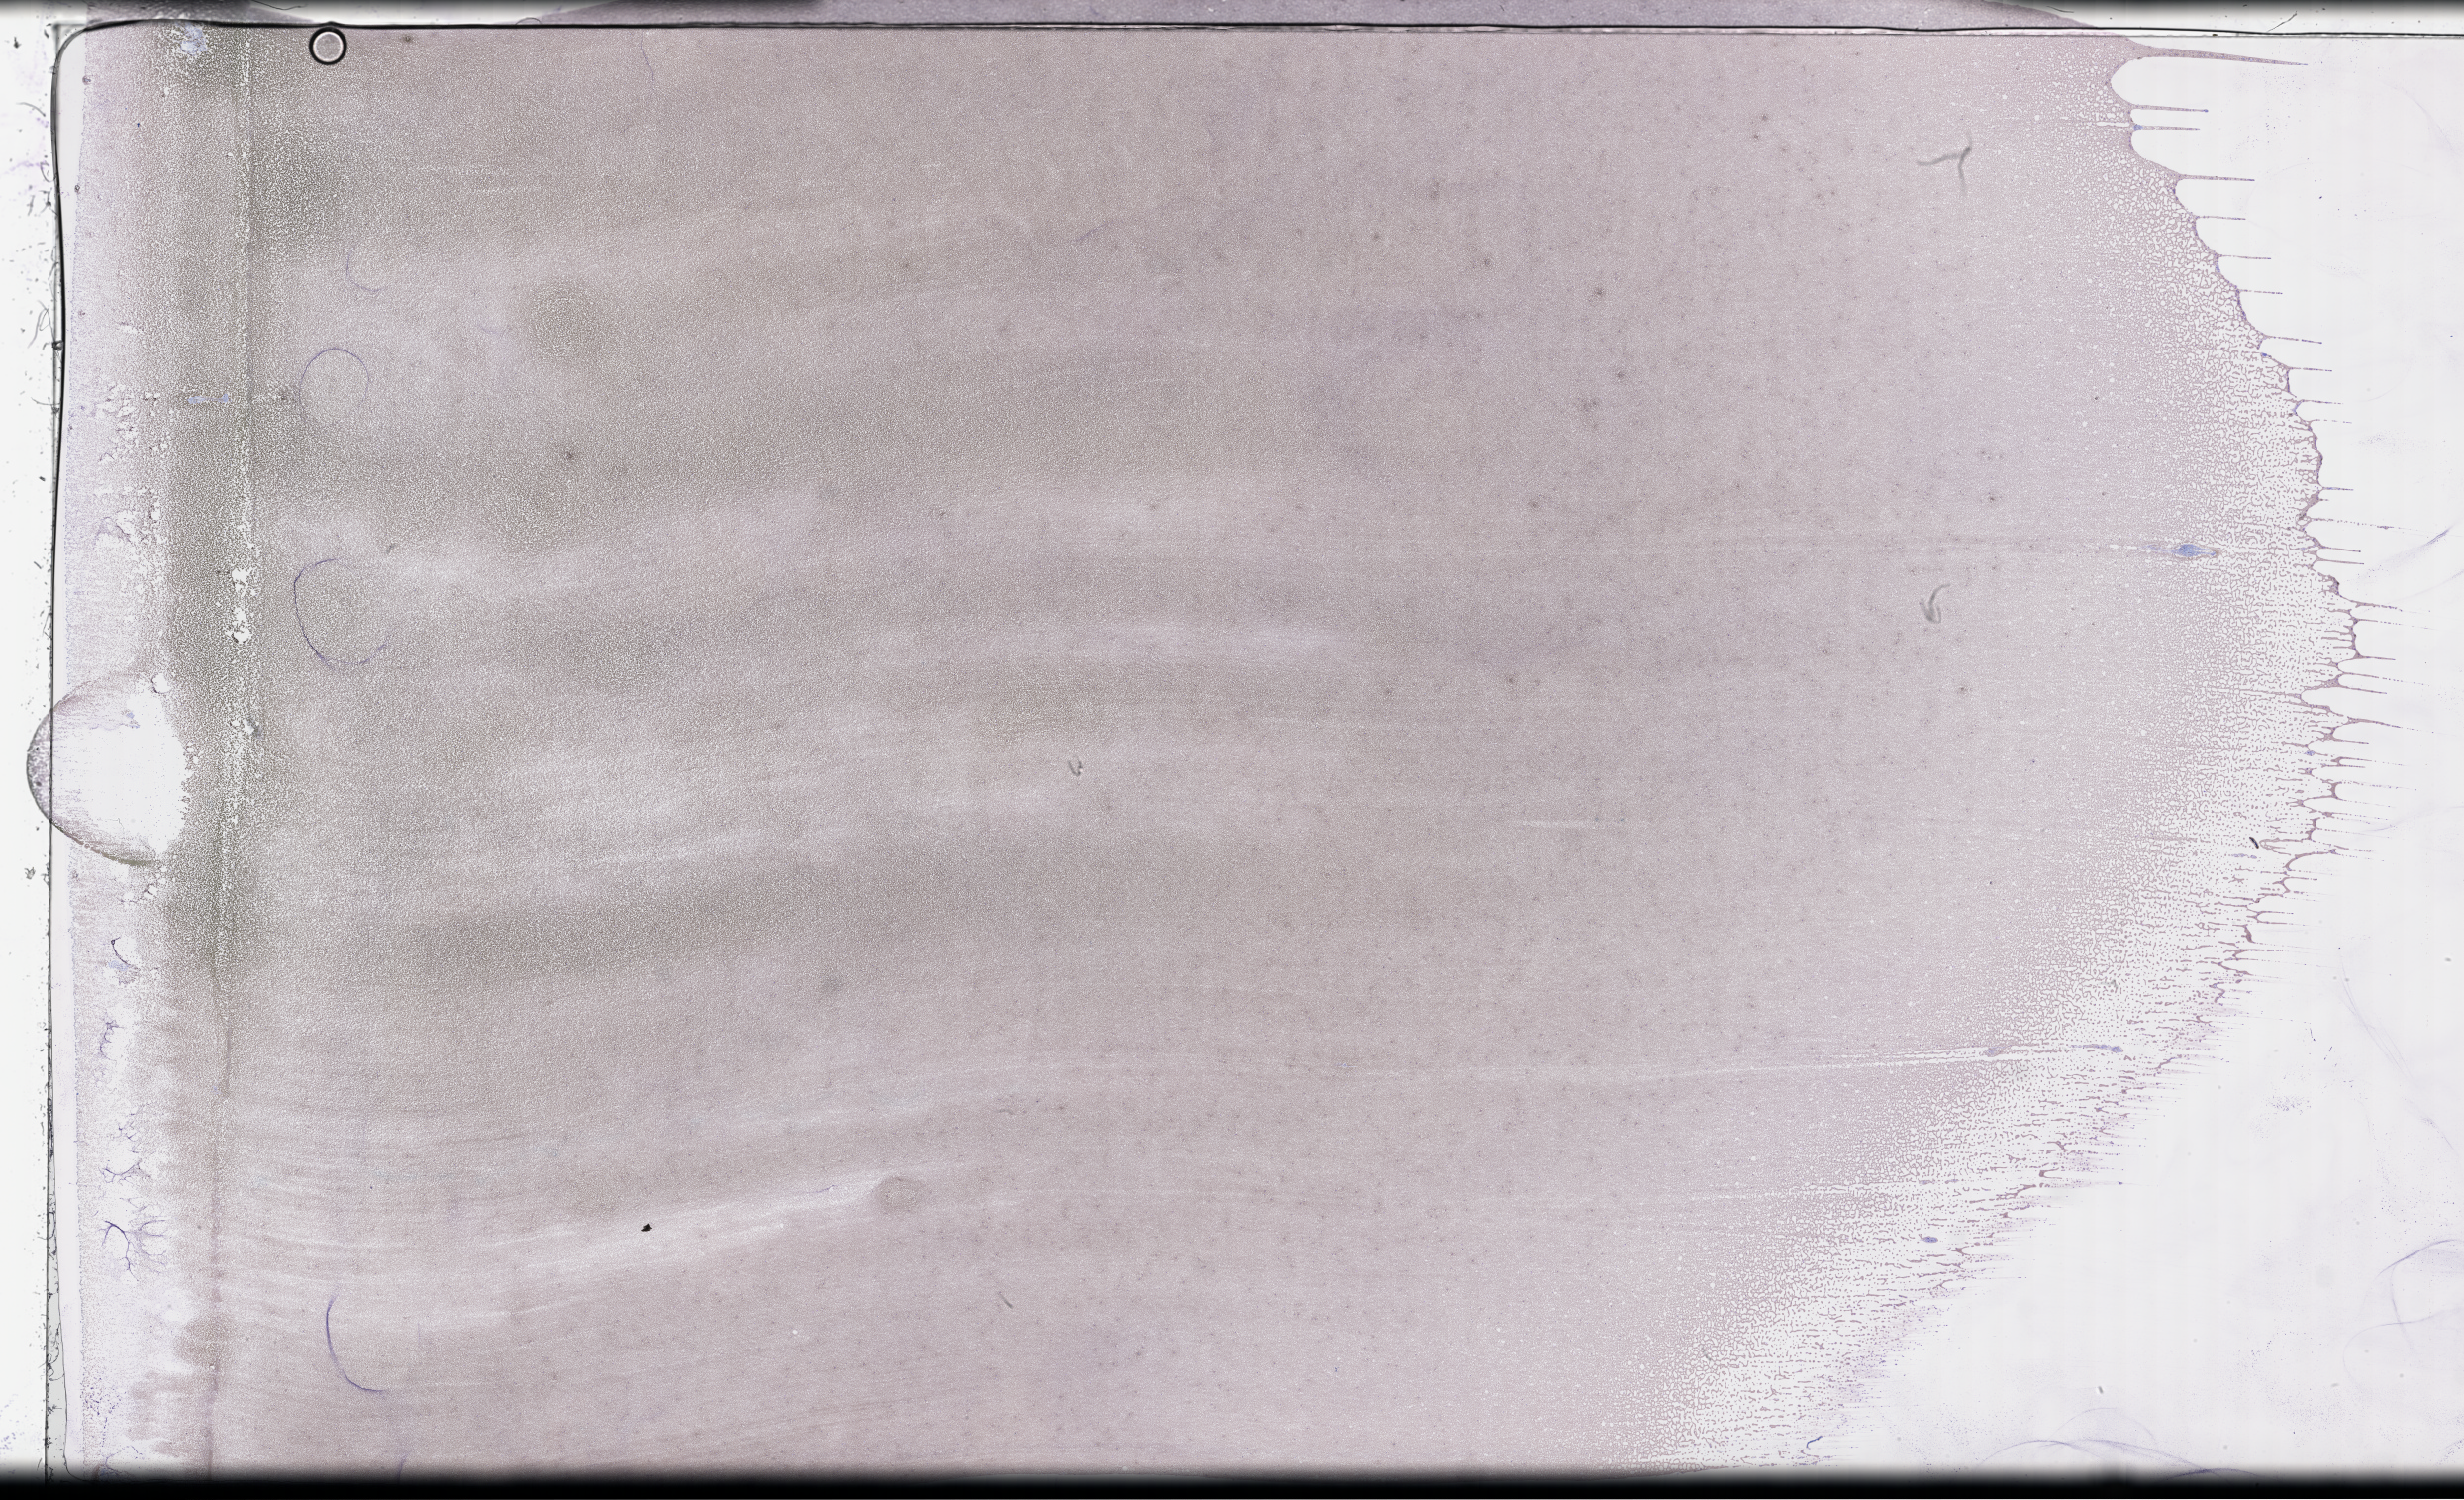
Wright-Giemsa-stained whole blood smear, whole-slide image — whole scanned area (about 40.2 x 24.5 mm) shown as a low-resolution overview; smear from an EDTA sample. Patient: male.
From a patient with: Plasma Cell Myeloma.